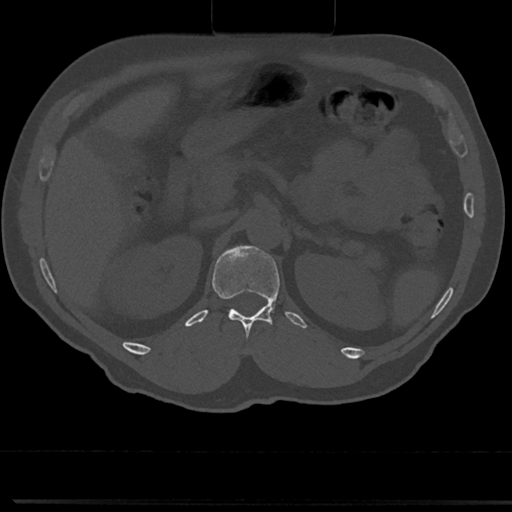
CT including the spine, one axial slice; slice 136 of 817 in the series (ordered by position); bone window (W 1800 / L 400 HU); 0.5 mm slice thickness; 512 × 512 image matrix, field of view 355 × 355 mm. Male patient, age 61 years. Case-level facts recorded for this patient, not image findings: primary cancer: prostate.
Outlined on this slice (semi-automatically segmented with operator editing):
- T12 vertebra: bounding box [x1, y1, x2, y2] px = [213, 260, 282, 357]